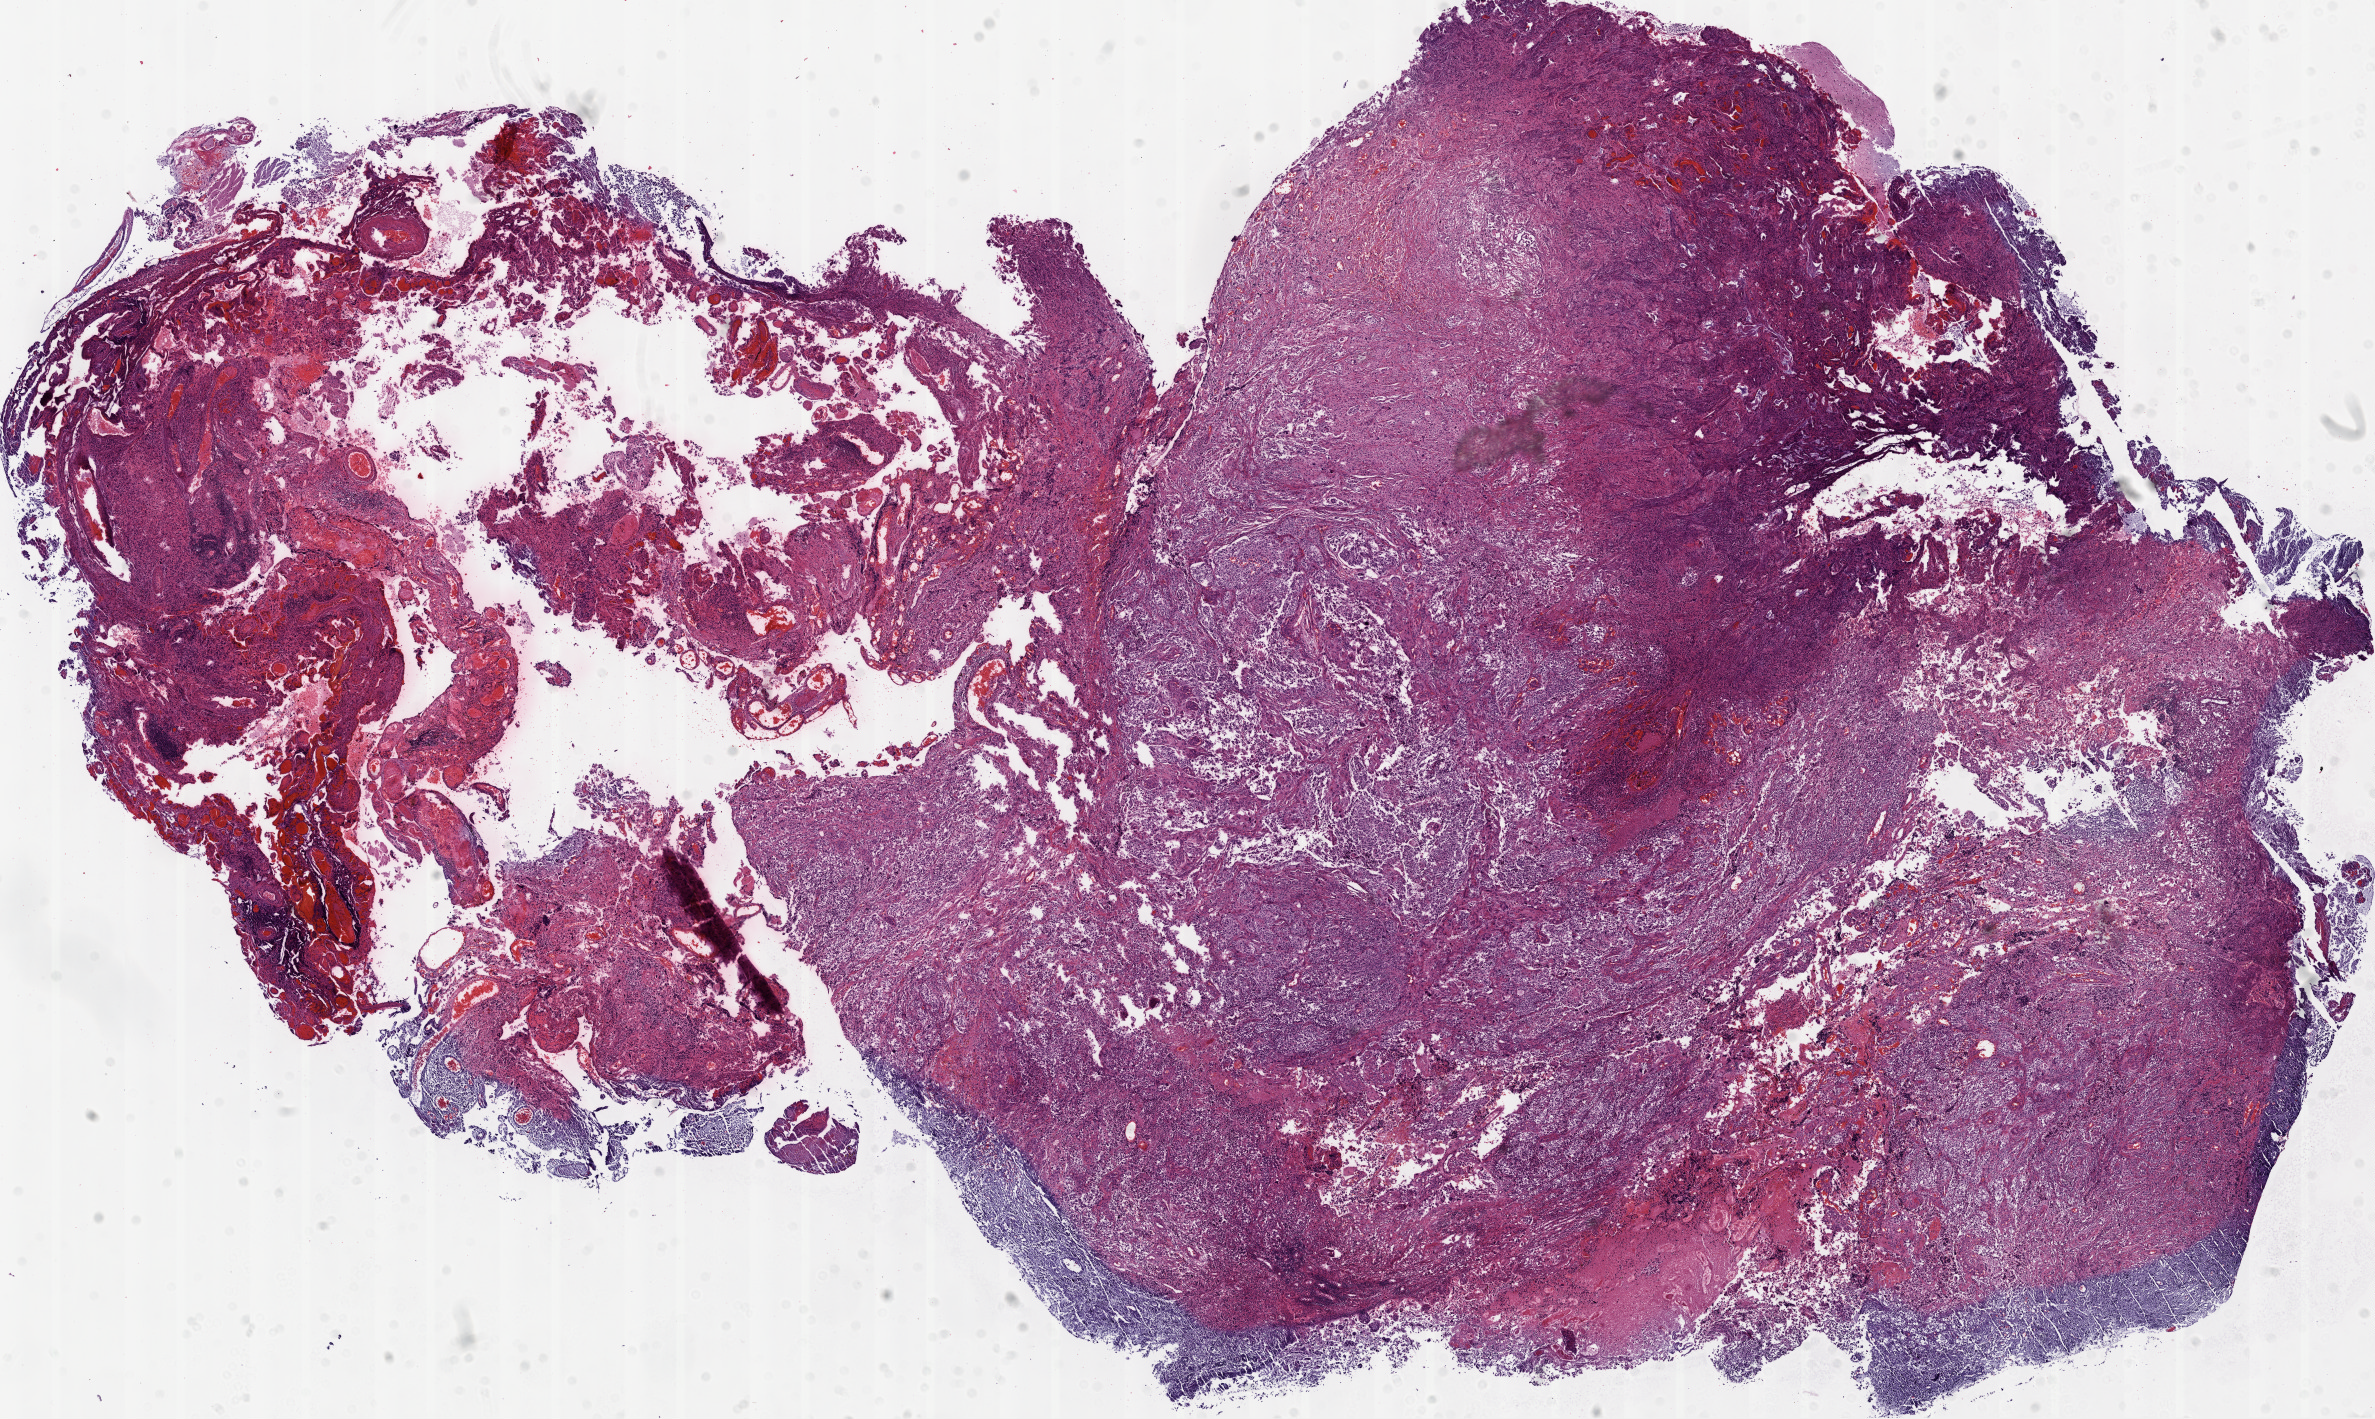
Whole-slide histology image, H&E-stained, shown as a low-resolution overview of the whole scanned area (about 19.1 x 11.4 mm); FFPE section; brain, primary tumour sample. Male patient; age at initial diagnosis 41 years.
• diagnosis: Glioblastoma